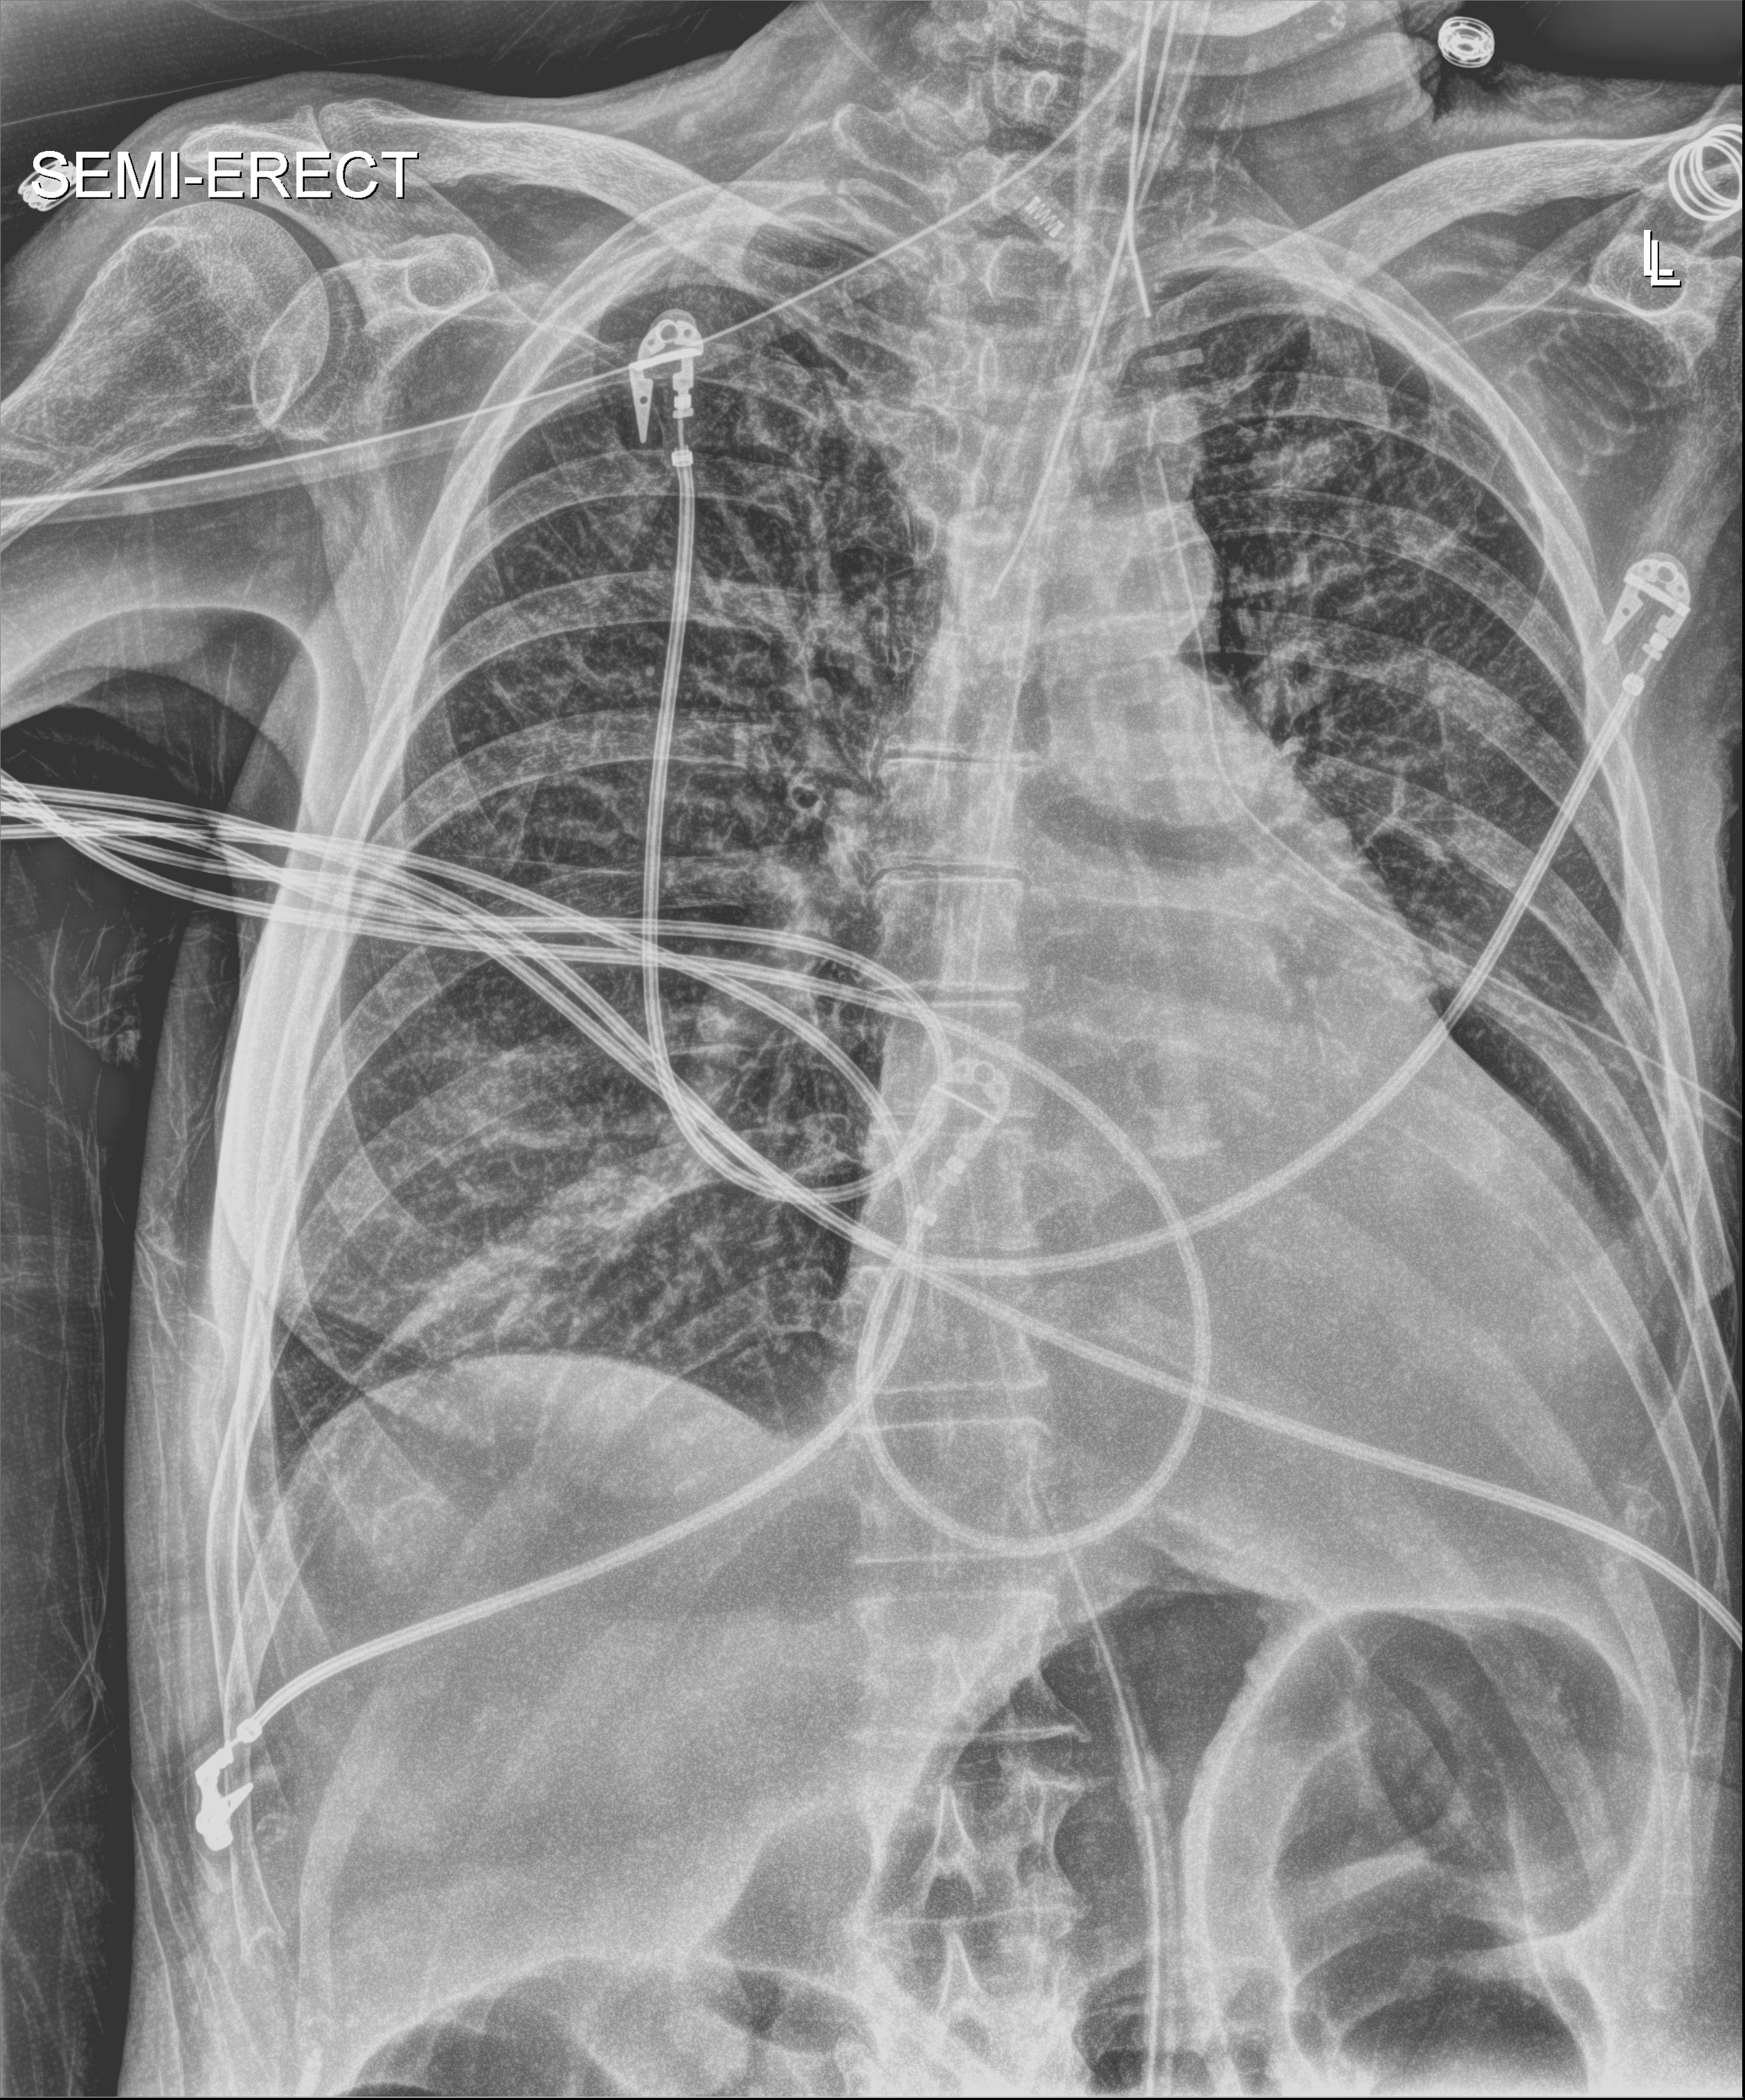
Portable chest radiograph, anteroposterior (AP) projection. Female patient hospitalised with COVID-19, age 60–74 years.
Admission-level facts for this patient (not findings on this image; timing relative to this image not recorded):
- length of hospital stay: 38 days
- mechanically ventilated during this hospital stay: yes
- admitted to intensive care during this hospital stay: yes